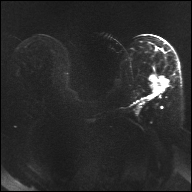
Breast MRI, one axial slice. Slice 16 of 32 in the series (ordered by position). Diffusion-weighted series; image 2 of 4 stored at this slice position (different b-values; order by instance number). 1.5 T. 4 mm slice thickness. 192 × 192 image matrix. Female patient.
Outlined on this slice (manually delineated by an expert):
- tumour on diffusion-weighted imaging: box from (x=150, y=75) to (x=168, y=93) px